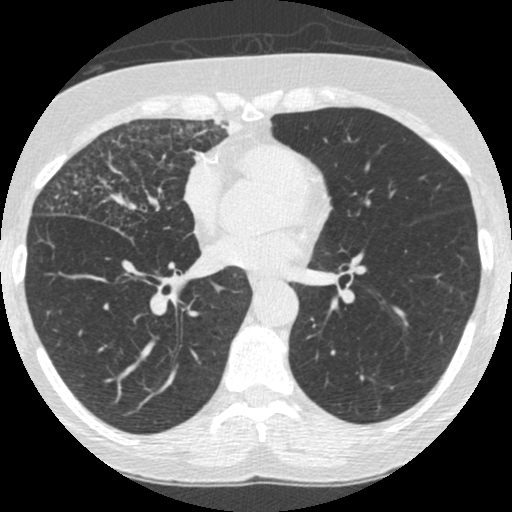
Low-dose screening chest CT, one axial slice. Position 123 of 253 along the scan axis. Lung window (W 1500 / L -600 HU). 1.25 mm slice thickness. 512 × 512 image matrix, field of view 294 × 294 mm.
Outlined on this slice (expert manual segmentation):
- lesion 4 (tumor, upper lobe of right lung): bounding box <191,116,242,154> (left, top, right, bottom; pixels)